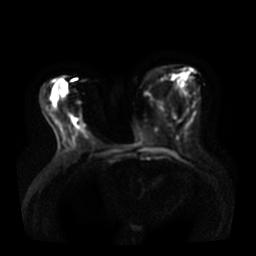
Breast MRI, one axial slice. Position 15 of 36 along the scan axis. Diffusion-weighted series; image 2 of 4 stored at this slice position (different b-values; order by instance number). 3 T. 5 mm slice thickness. 256 × 256 image matrix. Female patient.
Outlined on this slice (manually delineated by an expert):
- tumour on diffusion-weighted imaging: bounding box <73,119,76,123> (left, top, right, bottom; pixels)